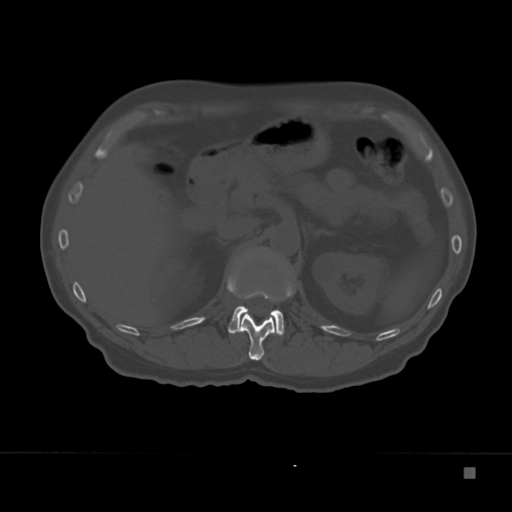
CT including the spine, one axial slice; slice 122 of 332 in the series (ordered by position); reconstruction kernel Br40s; bone window (W 1800 / L 400 HU); 1.5 mm slice thickness; 512 × 512 image matrix, field of view 389 × 389 mm. Patient: male, 72 years. Case-level facts recorded for this patient, not image findings: primary cancer: skeletal.
Outlined on this slice (semi-automatic segmentation, software-assisted and operator-edited):
- L1 vertebra: bounding box (x1, y1, x2, y2) in pixels: (228, 306, 284, 336)
- T12 vertebra: (227, 272, 295, 361)